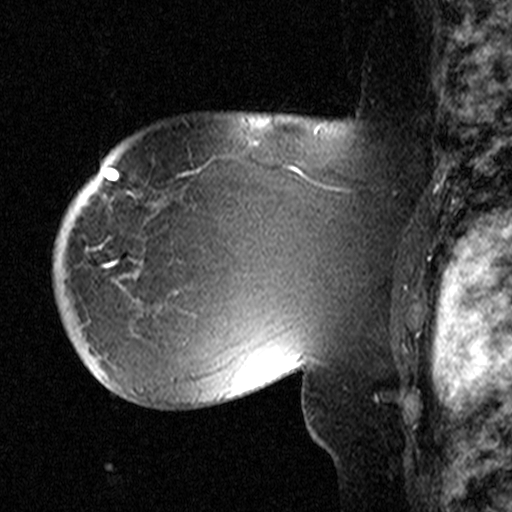
Breast MRI (dynamic contrast-enhanced), one sagittal slice. Slice 33 of 44 in the series (ordered by position). Dynamic contrast-enhanced study with each time point stored as its own series, time point 2 of 3 at this slice position (early post-contrast, ordered by acquisition time). 1.5 T. TE 4.5 ms, TR 11 ms. 3.27 mm slice thickness. 512 × 512 image matrix, field of view 200 × 200 mm. Female patient, age 53 years. Case-level facts recorded for this patient, not image findings: setting: breast cancer imaged before/during neoadjuvant chemotherapy; receptor status: HR-positive, HER2-negative.
Structures marked on this image (semi-automatically segmented with operator editing):
- analysis volume of interest (the breast-tissue region the enhancement analysis was run in; not a lesion): bounding box <58,154,311,367> (left, top, right, bottom; pixels)
- tumour enhancement mask (voxels above the 90 % enhancement threshold inside the analysis volume of interest): <97,247,115,267>